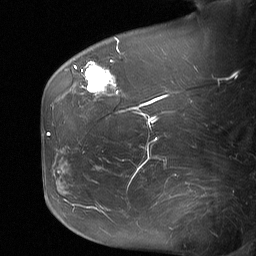
Breast MRI (dynamic contrast-enhanced), one sagittal slice. Position 20 of 64 along the scan axis. Dynamic contrast-enhanced study with each time point stored as its own series, time point 2 of 3 at this slice position (early post-contrast, ordered by acquisition time). 1.5 T. TE 4.8 ms, TR 27 ms. 2 mm slice thickness. 256 × 256 image matrix. Female patient, age 60 years. Case-level facts recorded for this patient, not image findings: setting: breast cancer imaged before/during neoadjuvant chemotherapy; receptor status: HR-positive, HER2-negative.
Outlined on this slice (semi-automatically segmented with operator editing):
- analysis volume of interest (the breast-tissue region the enhancement analysis was run in; not a lesion): bounding box (x1, y1, x2, y2) in pixels: (79, 50, 122, 99)
- tumour enhancement mask (voxels above the 90 % enhancement threshold inside the analysis volume of interest): (82, 61, 118, 93)